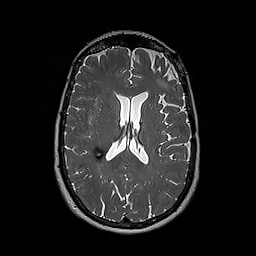
Brain MRI from a brain-tumour surgery series, one axial slice. Slice 108 of 192 in the series (ordered by position). 256 × 256 image matrix. Case-level facts recorded for this patient, not image findings: histopathology: Oligodendroglioma; WHO grade: 2; IDH mutation: yes; tumour location: Left Frontal.
Annotated regions visible in this slice (manually delineated by an expert):
- tumour: box from (x=157, y=80) to (x=160, y=85) px